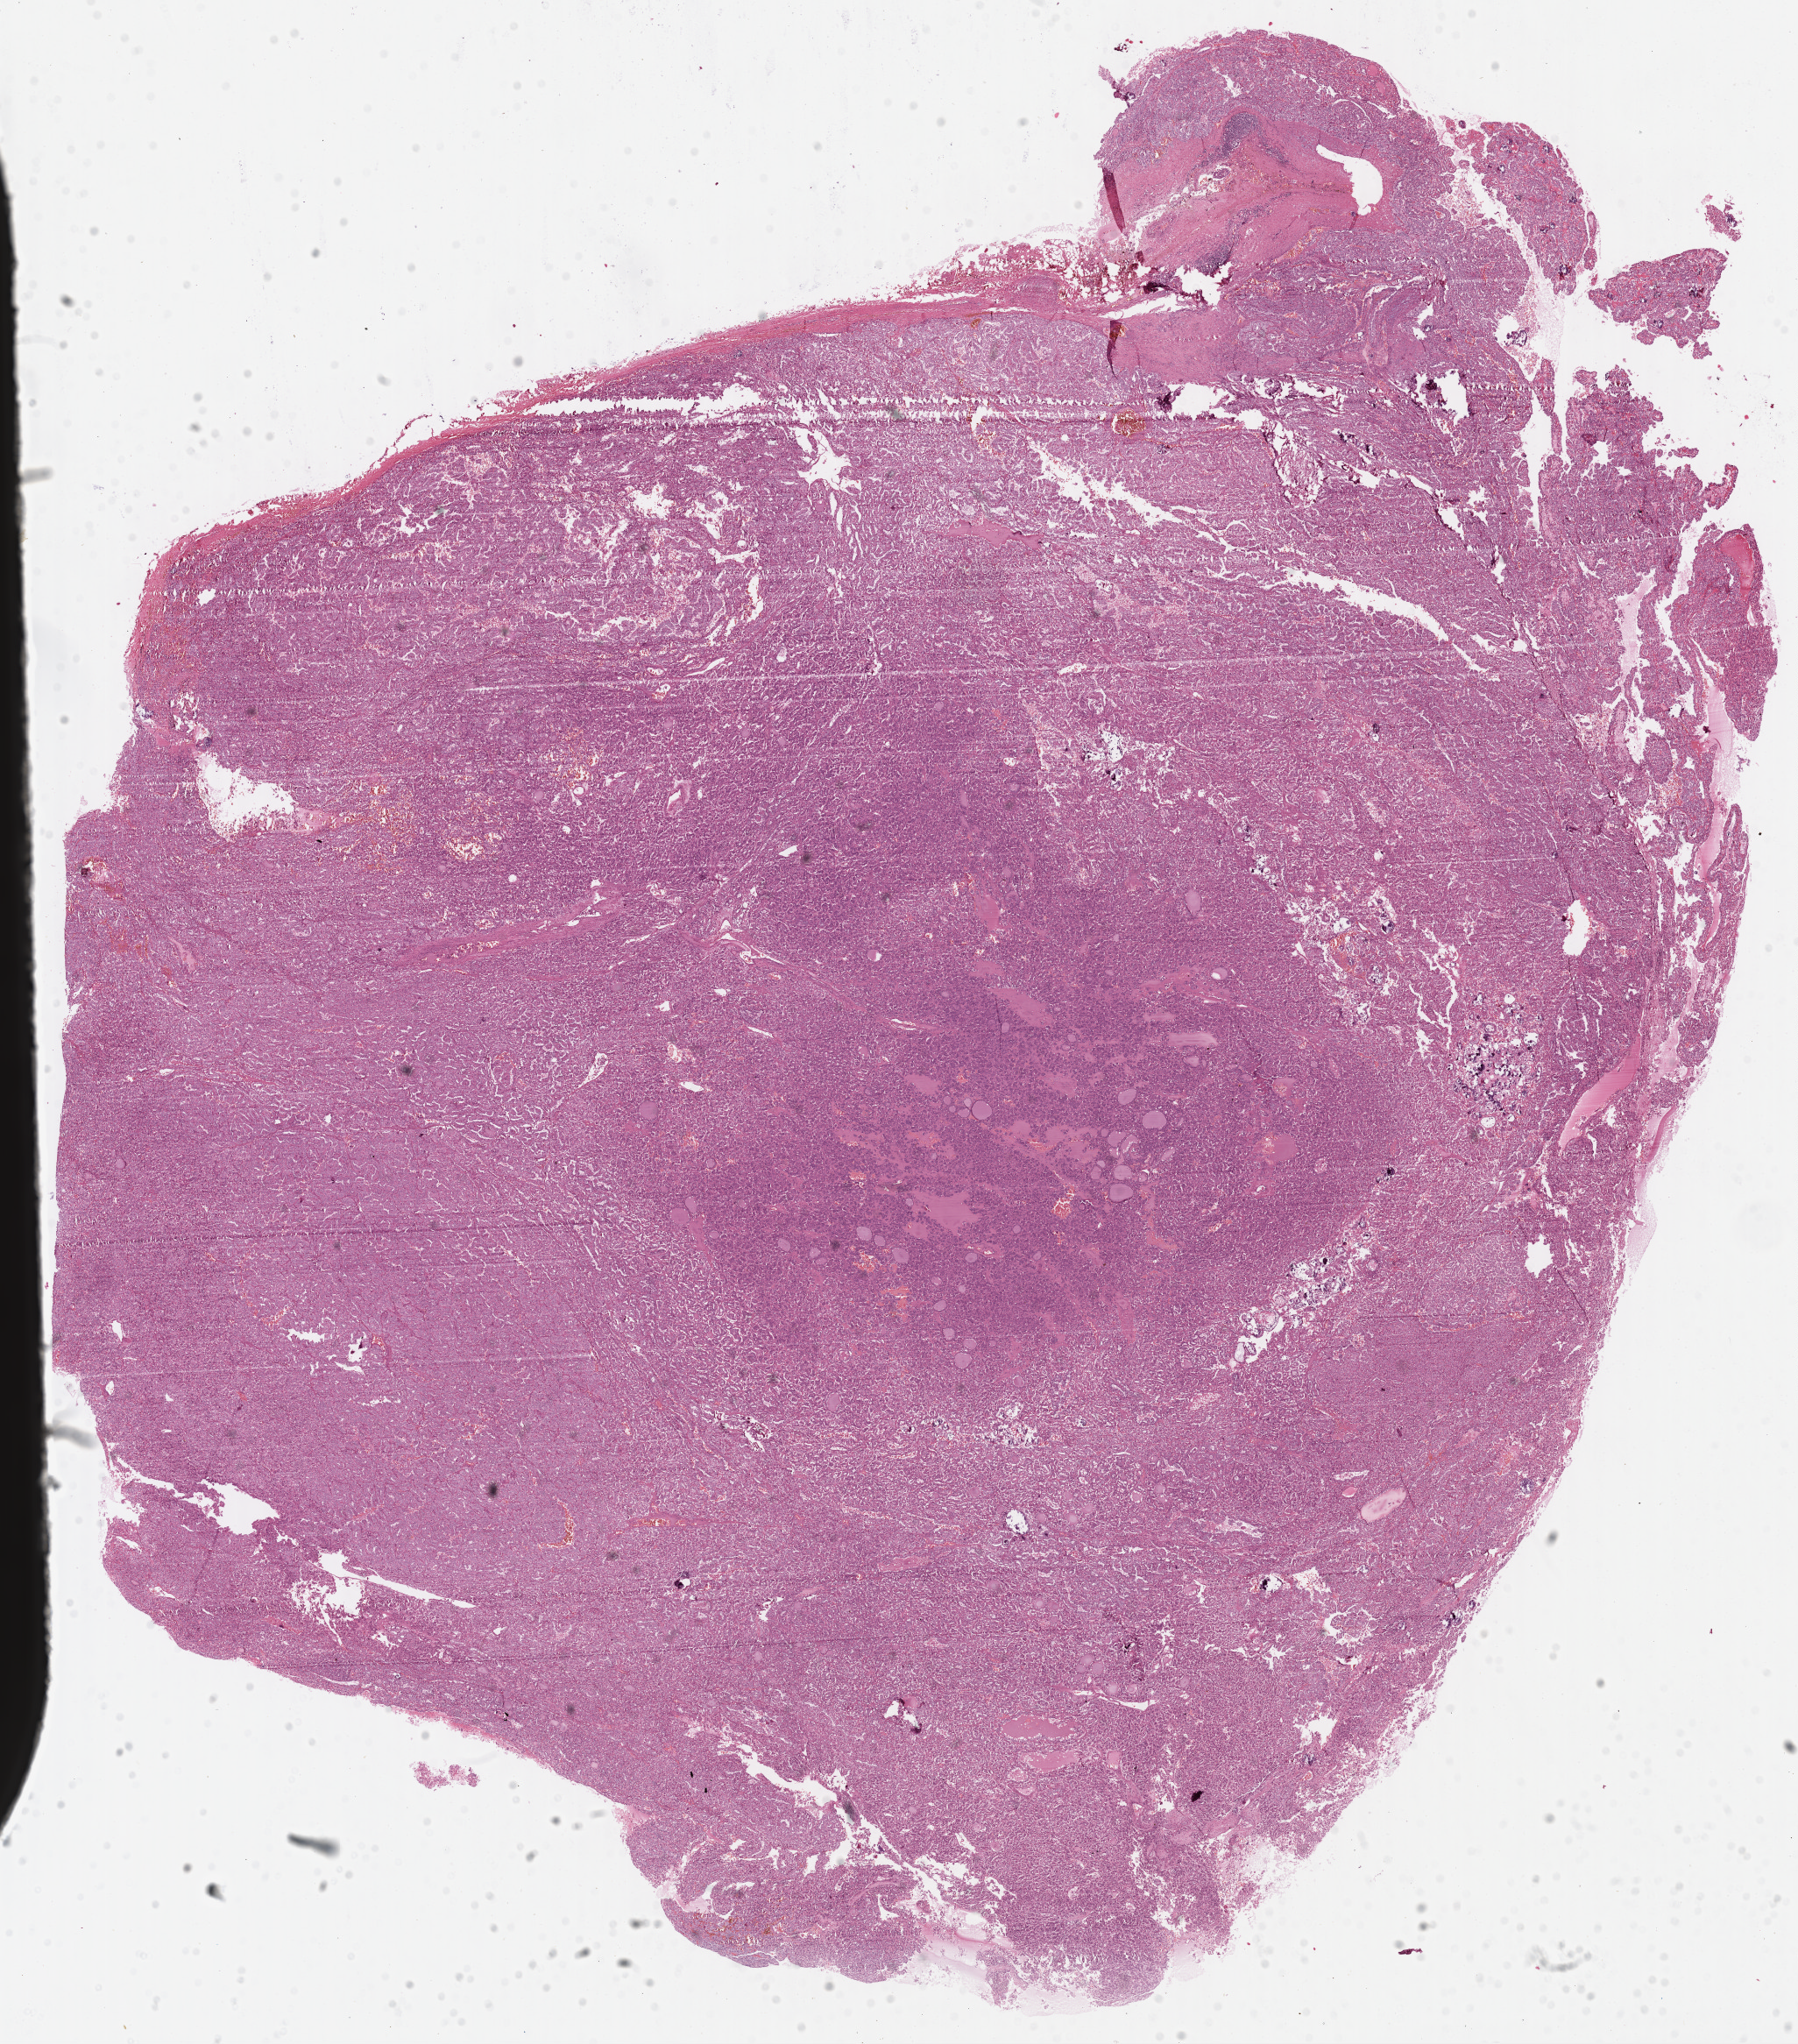
Digitized H&E-stained tissue section (whole slide) — low-resolution overview of the scanned area, about 16.2 x 18.4 mm (from a 40x scan). Formalin-fixed paraffin-embedded (FFPE) diagnostic section. Sample: primary tumour, thyroid. Female patient; age at initial diagnosis 30 years.
• histologic diagnosis: Papillary adenocarcinoma, NOS (thyroid gland)
• AJCC pathologic stage: I
• lymph nodes positive (case pathology): 2 of 2 examined
• TNM: T3 N1 M0